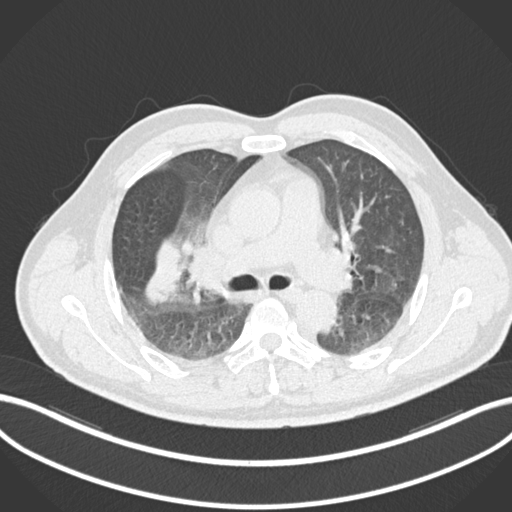
Chest CT, one axial slice; slice 641 of 852 in the series (ordered by position); 120 kVp; lung window (W 1500 / L -600 HU); 1 mm slice thickness; 512 × 512 image matrix, field of view 400 × 400 mm. Male patient, age 55 years. From the clinical record (not read from this slice): clinical TNM (as recorded): T3 N2 M1.
Structures marked on this image (rectangle marked by the reading radiologist):
- lung tumour (recorded histology: adenocarcinoma): bounding box (x1, y1, x2, y2) in pixels: (139, 237, 185, 309)